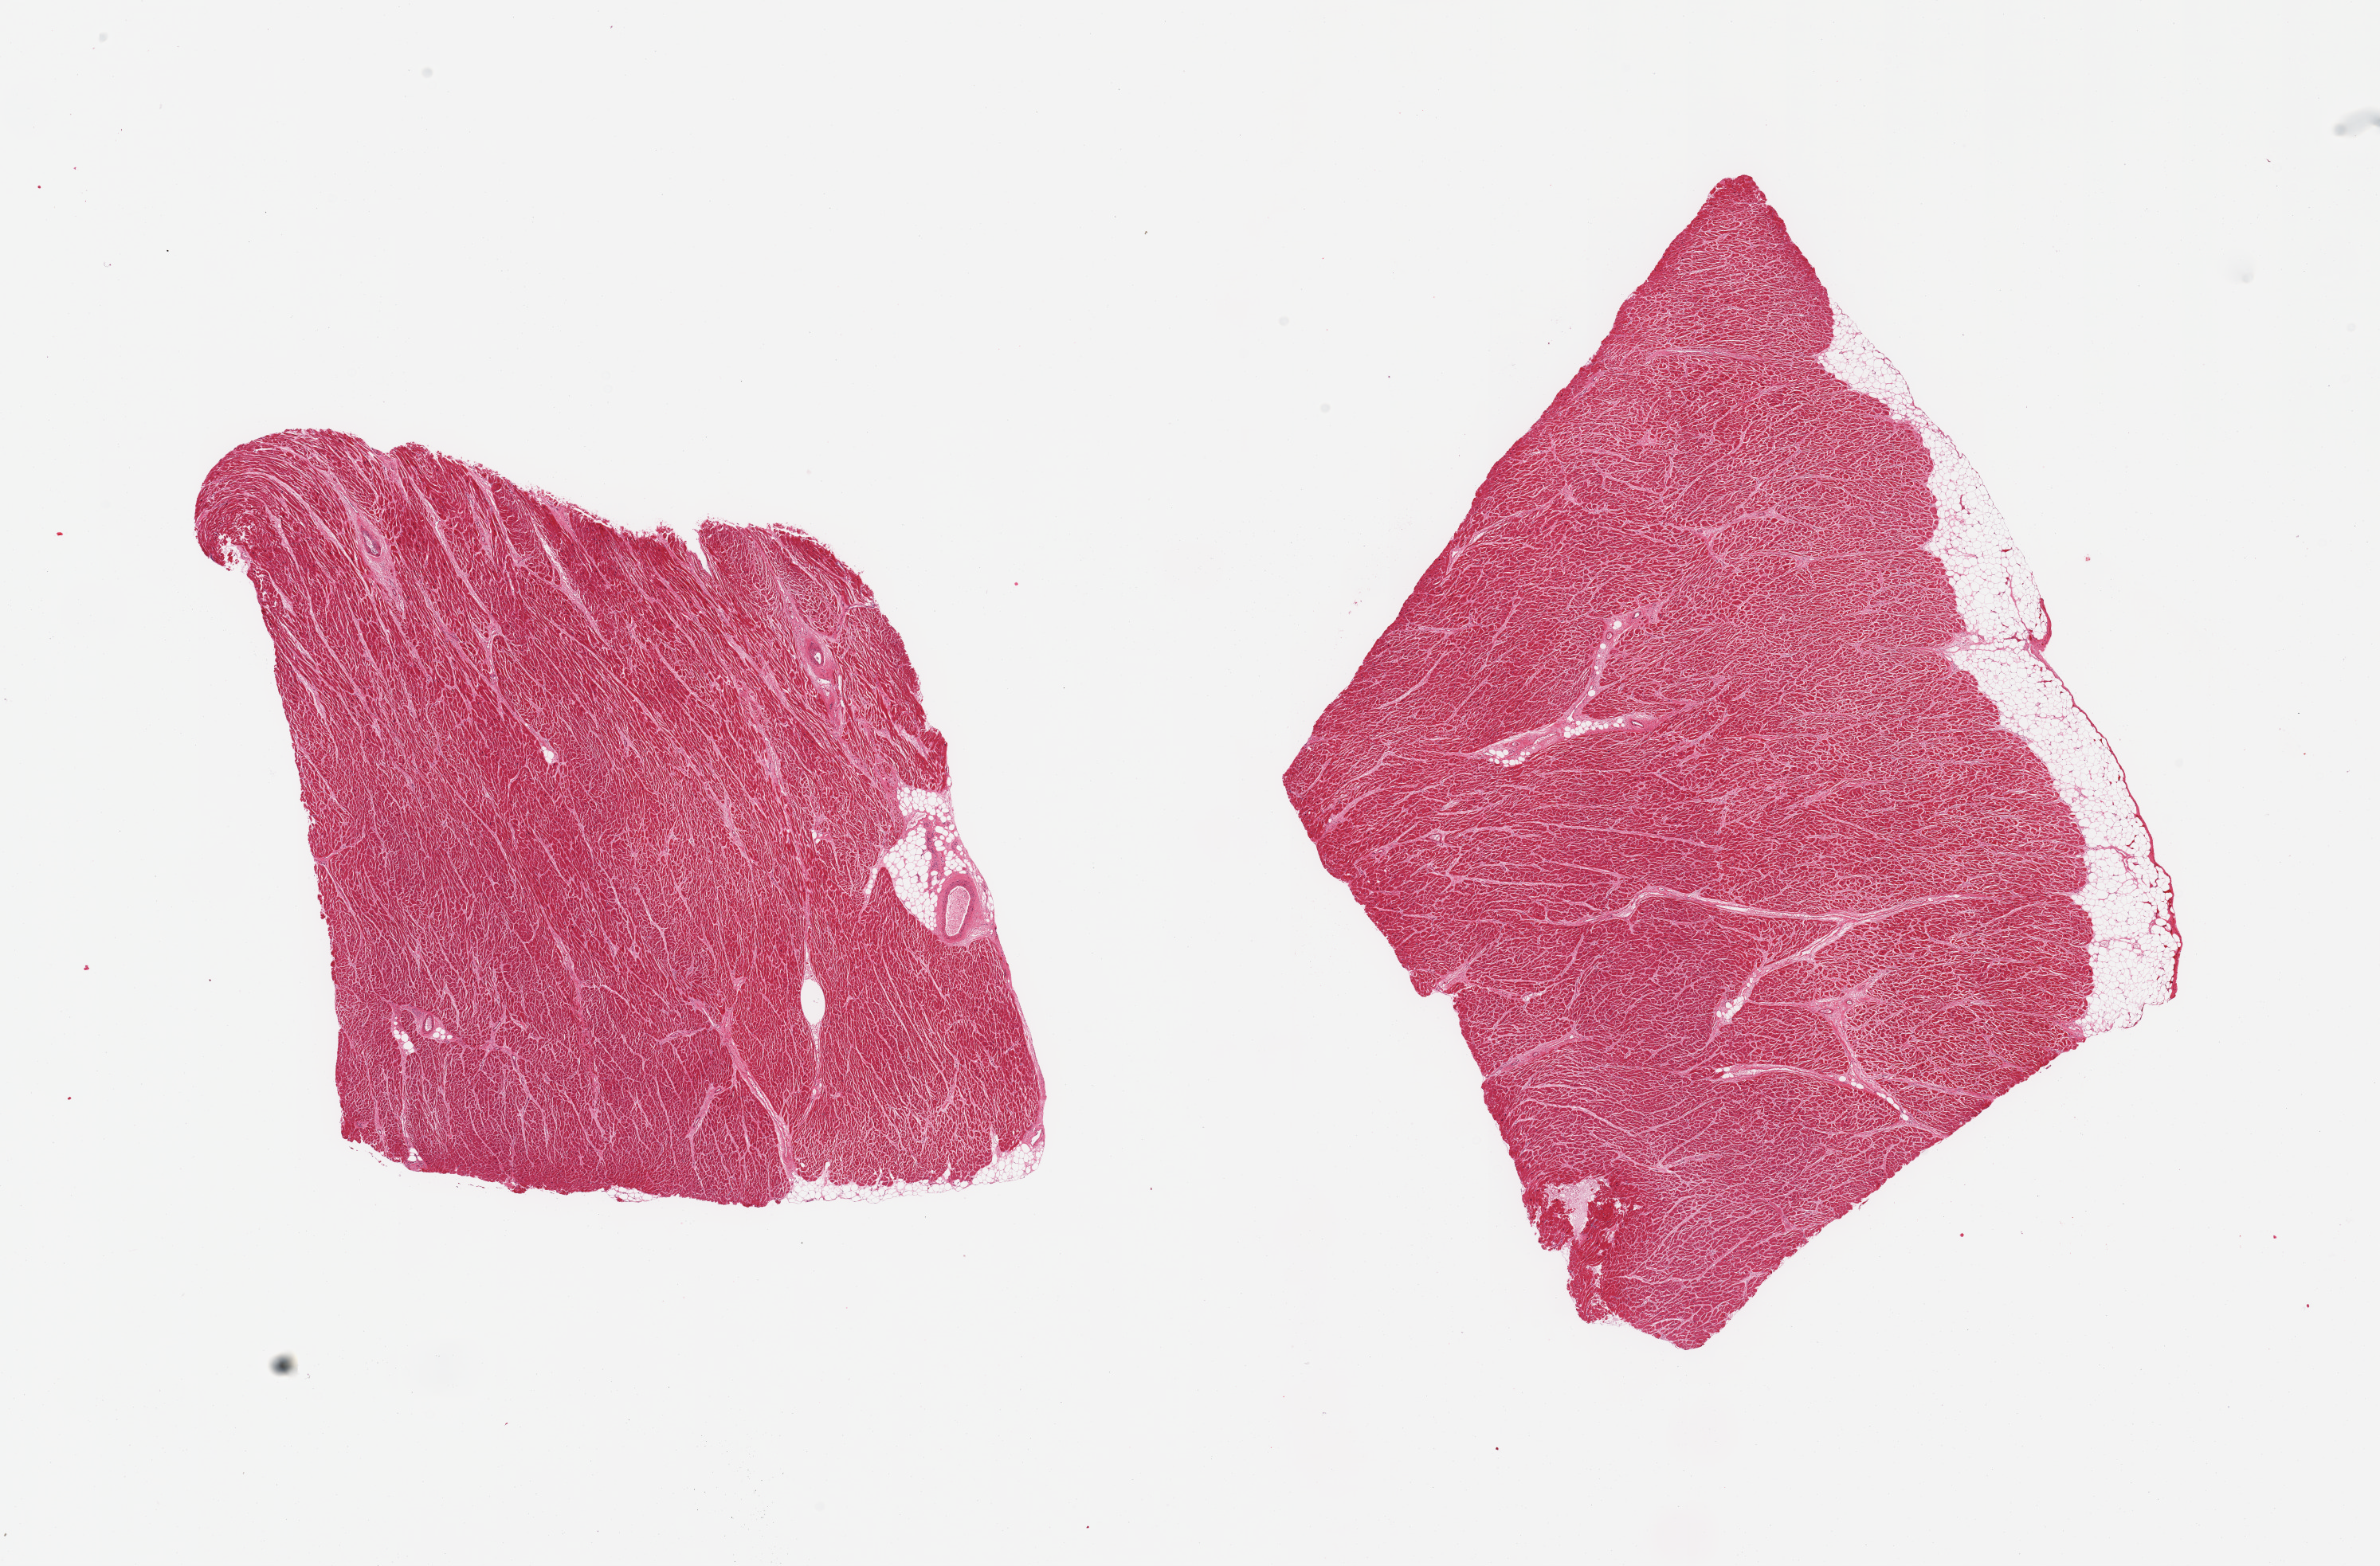
Whole-slide image, haematoxylin and eosin stain, low-resolution overview of the scanned area, about 23.6 x 15.6 mm (slide scanned at 20x); PAXgene-fixed paraffin-embedded (PFPE) section; section of heart (target tissue); tissue donor sample. Donor: male.
• review note (as recorded): 2 pieces; perivascular fat; mild interstitial fibrosis; one piece with ~1mm rim of fat